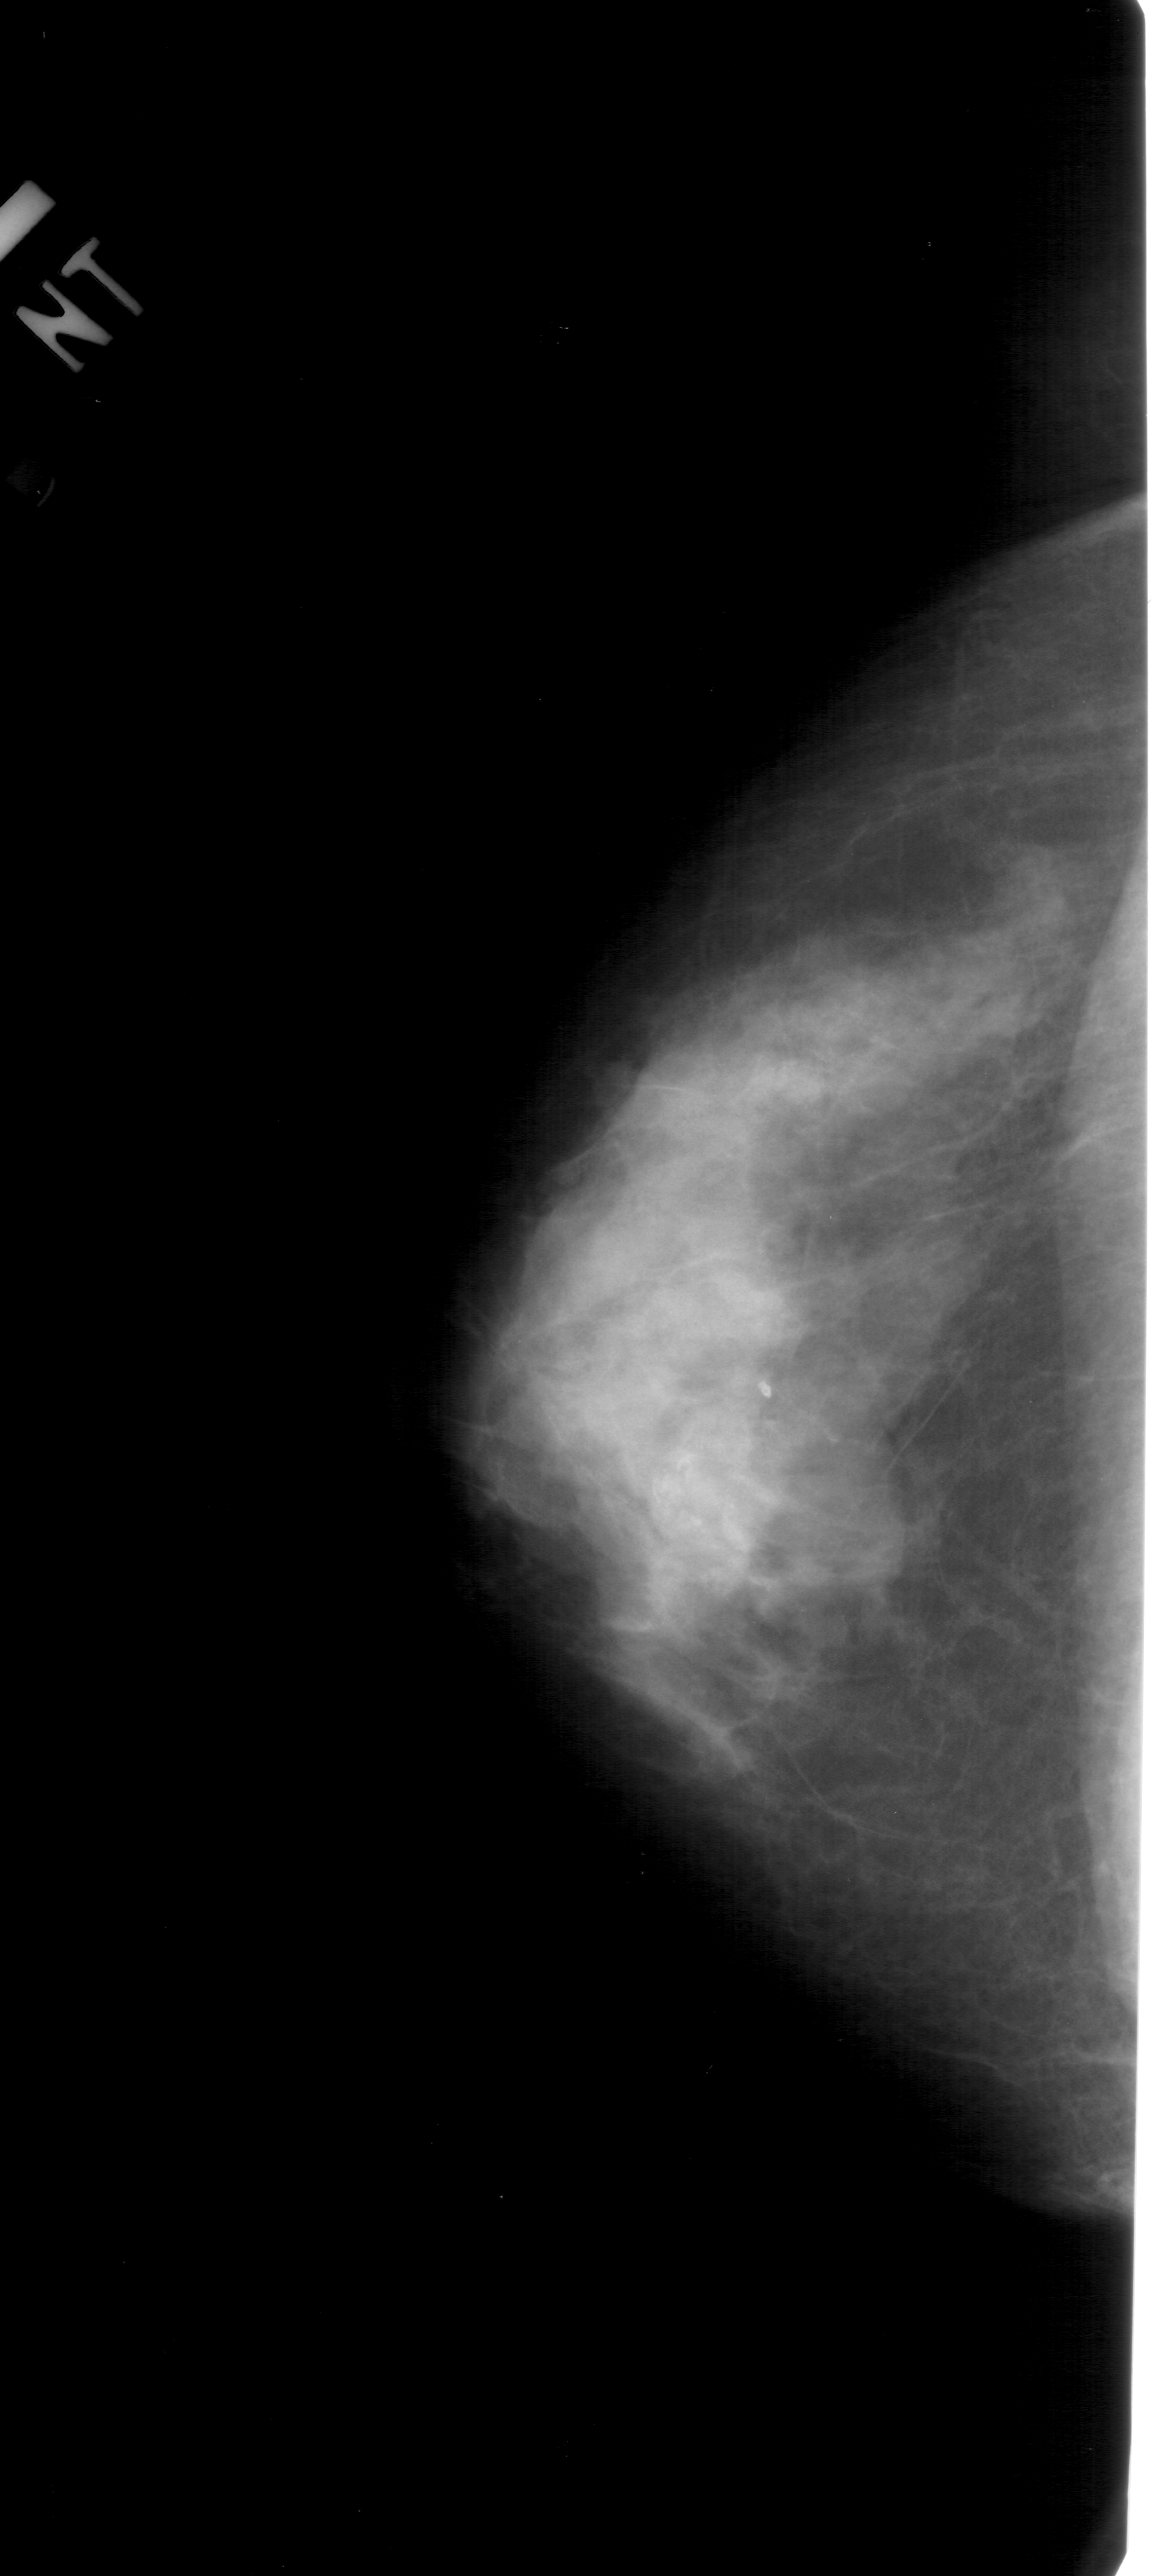
Mammogram (digitized film). Left breast. CC view. BI-RADS breast density category 4 (scale 1–4). 1155 × 2576 image matrix.
Marked abnormalities (boxes around the expert regions of interest):
- calcifications, morphology pleomorphic, distribution clustered; BI-RADS assessment category 4; pathology result (as recorded, not read from the image): malignant: box from (x=645, y=1448) to (x=766, y=1564) px